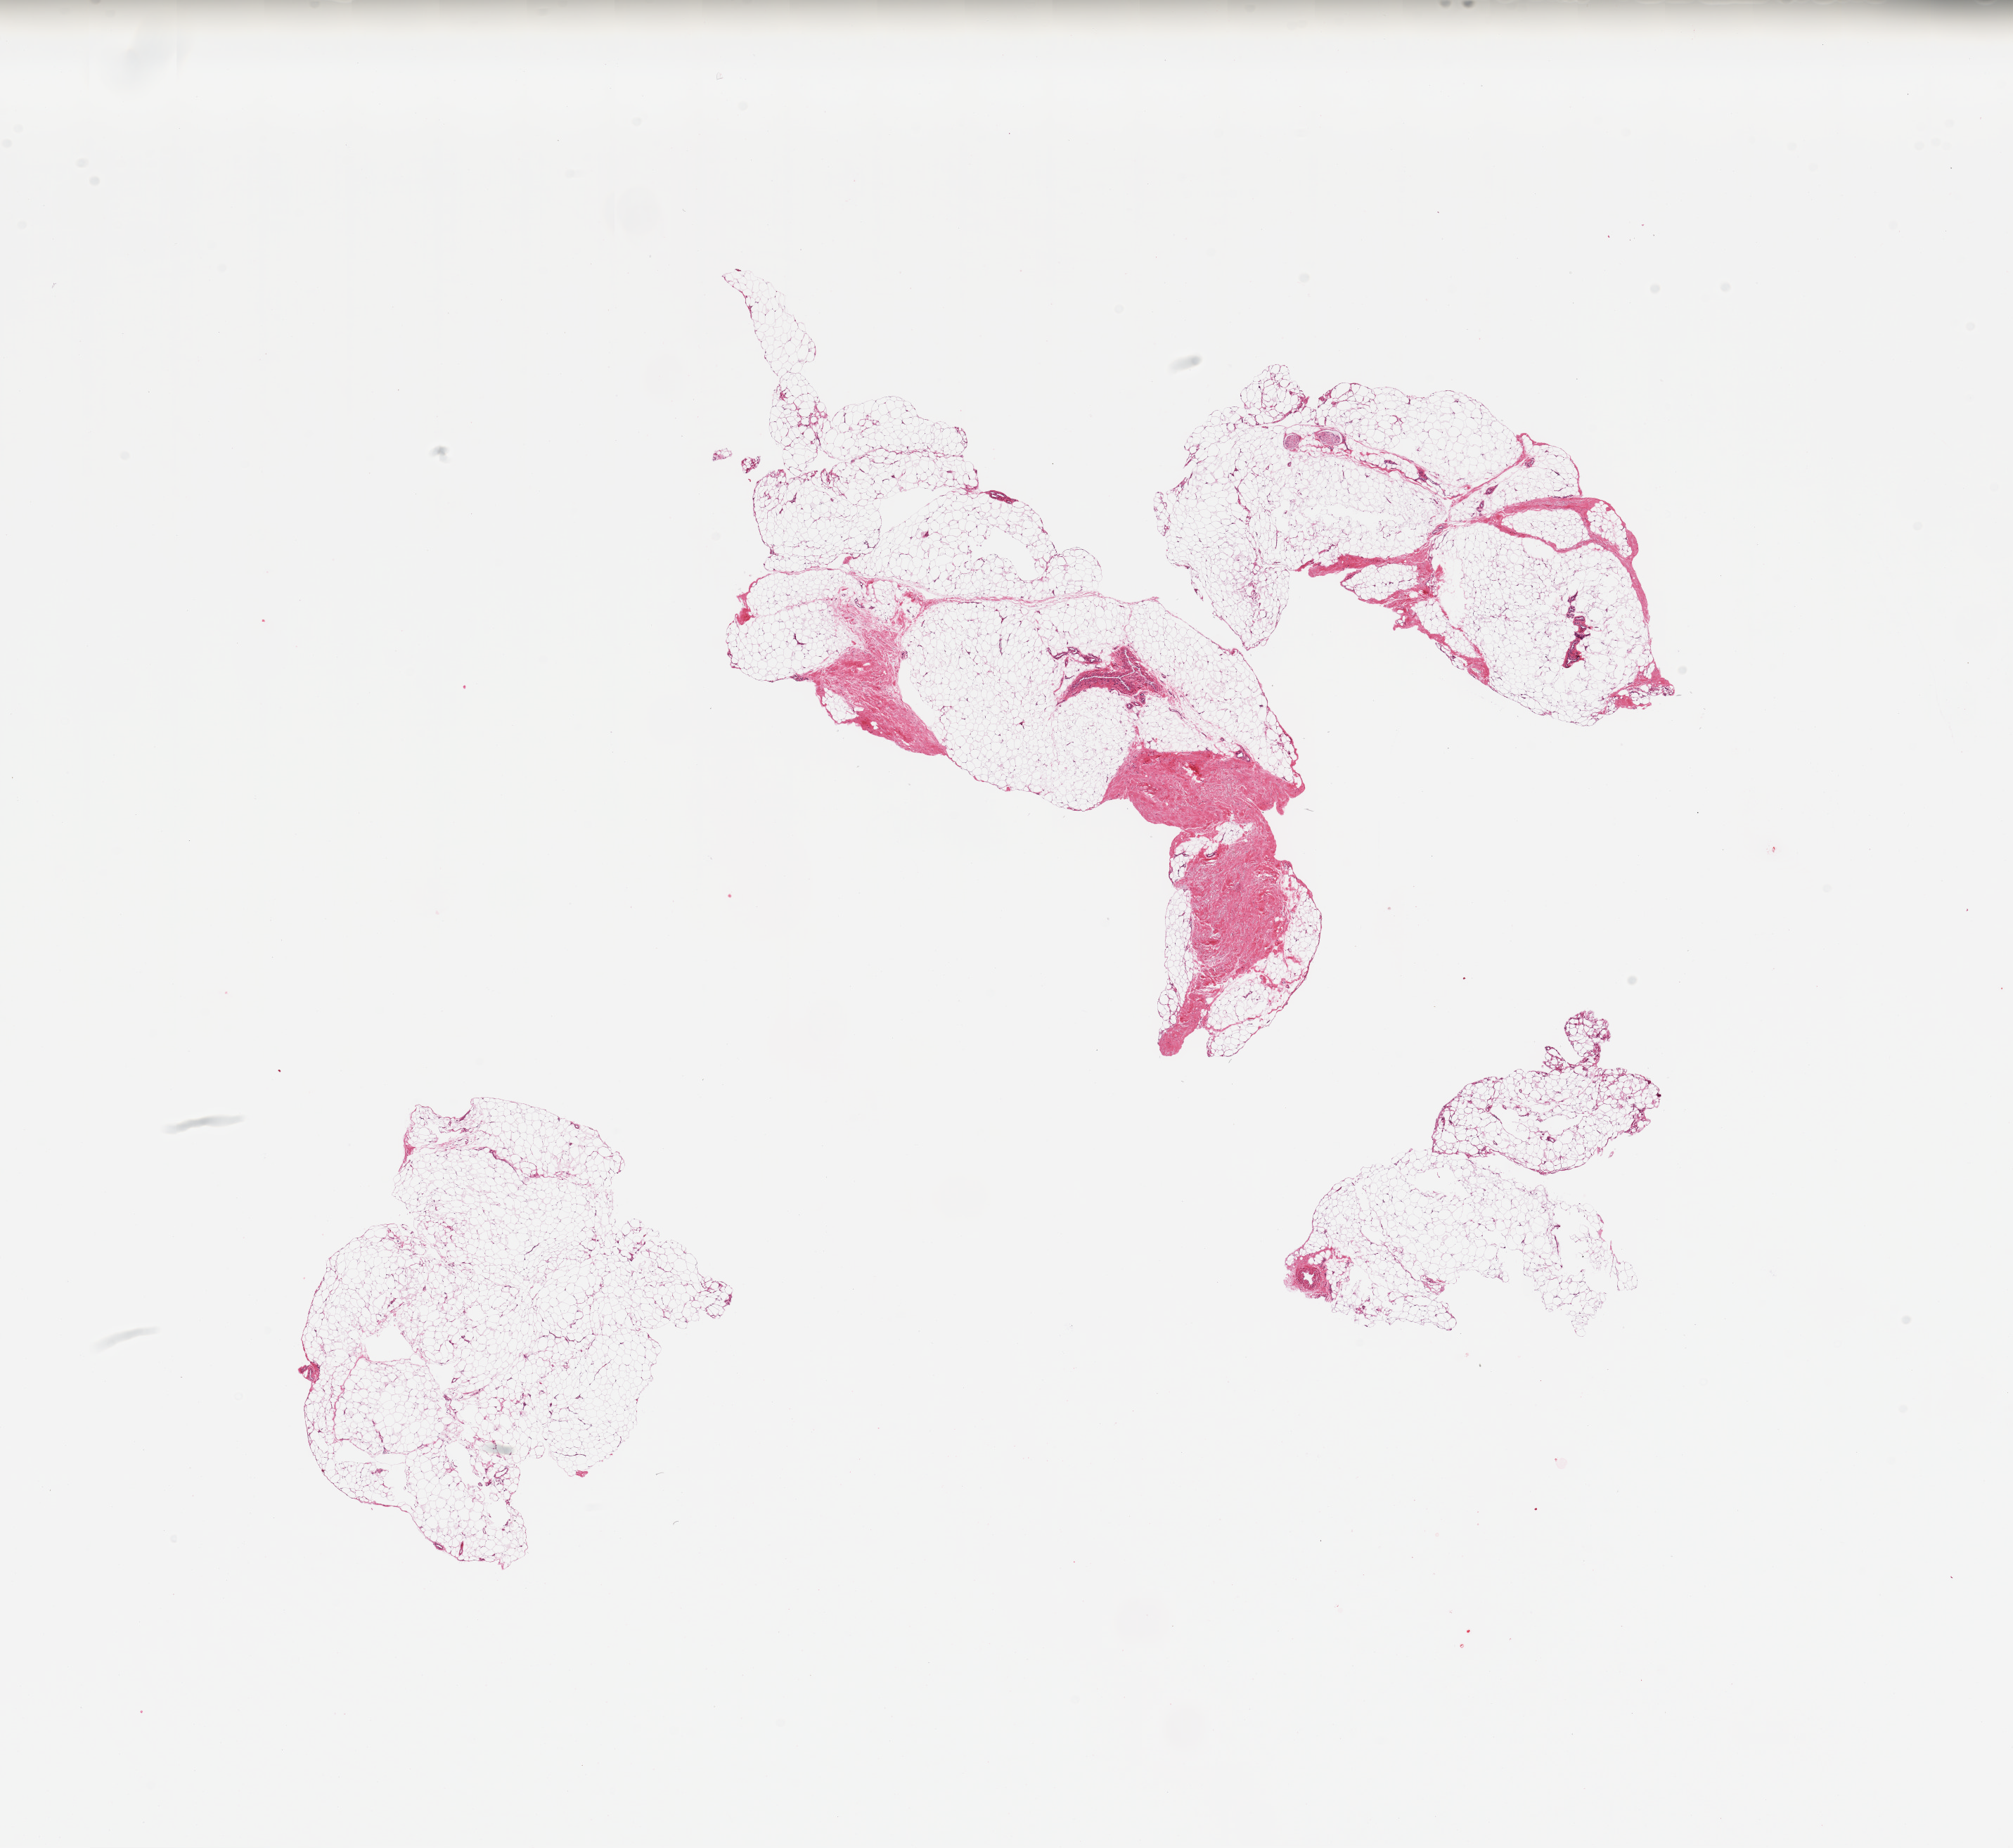
Whole-slide image, H&E stain, shown as a low-resolution overview of the whole scanned area (about 22.6 x 20.8 mm). PAXgene-fixed paraffin-embedded (PFPE) section. Sampled site (target tissue): adipose tissue. Tissue donor sample. Donor: male.
Reviewer comment on this tissue sample: 2 pieces; mature adipose tissue, fibrovascular component and nerves.